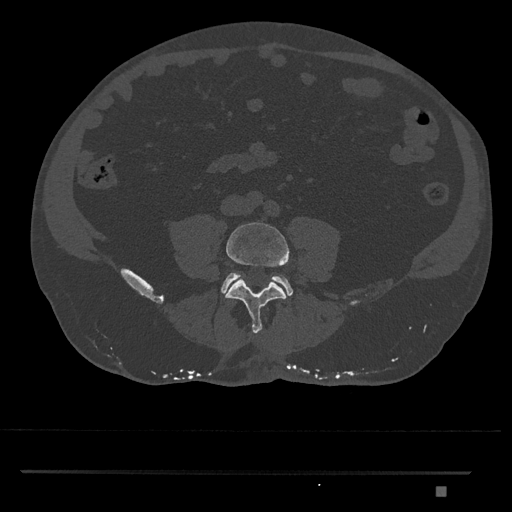
CT including the spine, one axial slice; slice 598 of 1134 in the series (ordered by position); reconstruction kernel Br40s/3; 120 kVp; bone window (W 1800 / L 400 HU); 512 × 512 image matrix, field of view 429 × 429 mm. Patient: male, 65 years. Case-level facts recorded for this patient, not image findings: primary cancer: prostate.
Outlined on this slice (semi-automatic segmentation, software-assisted and operator-edited):
- L4 vertebra: box from (x=225, y=222) to (x=289, y=334) px
- L5 vertebra: (x=221, y=273)–(x=293, y=296)